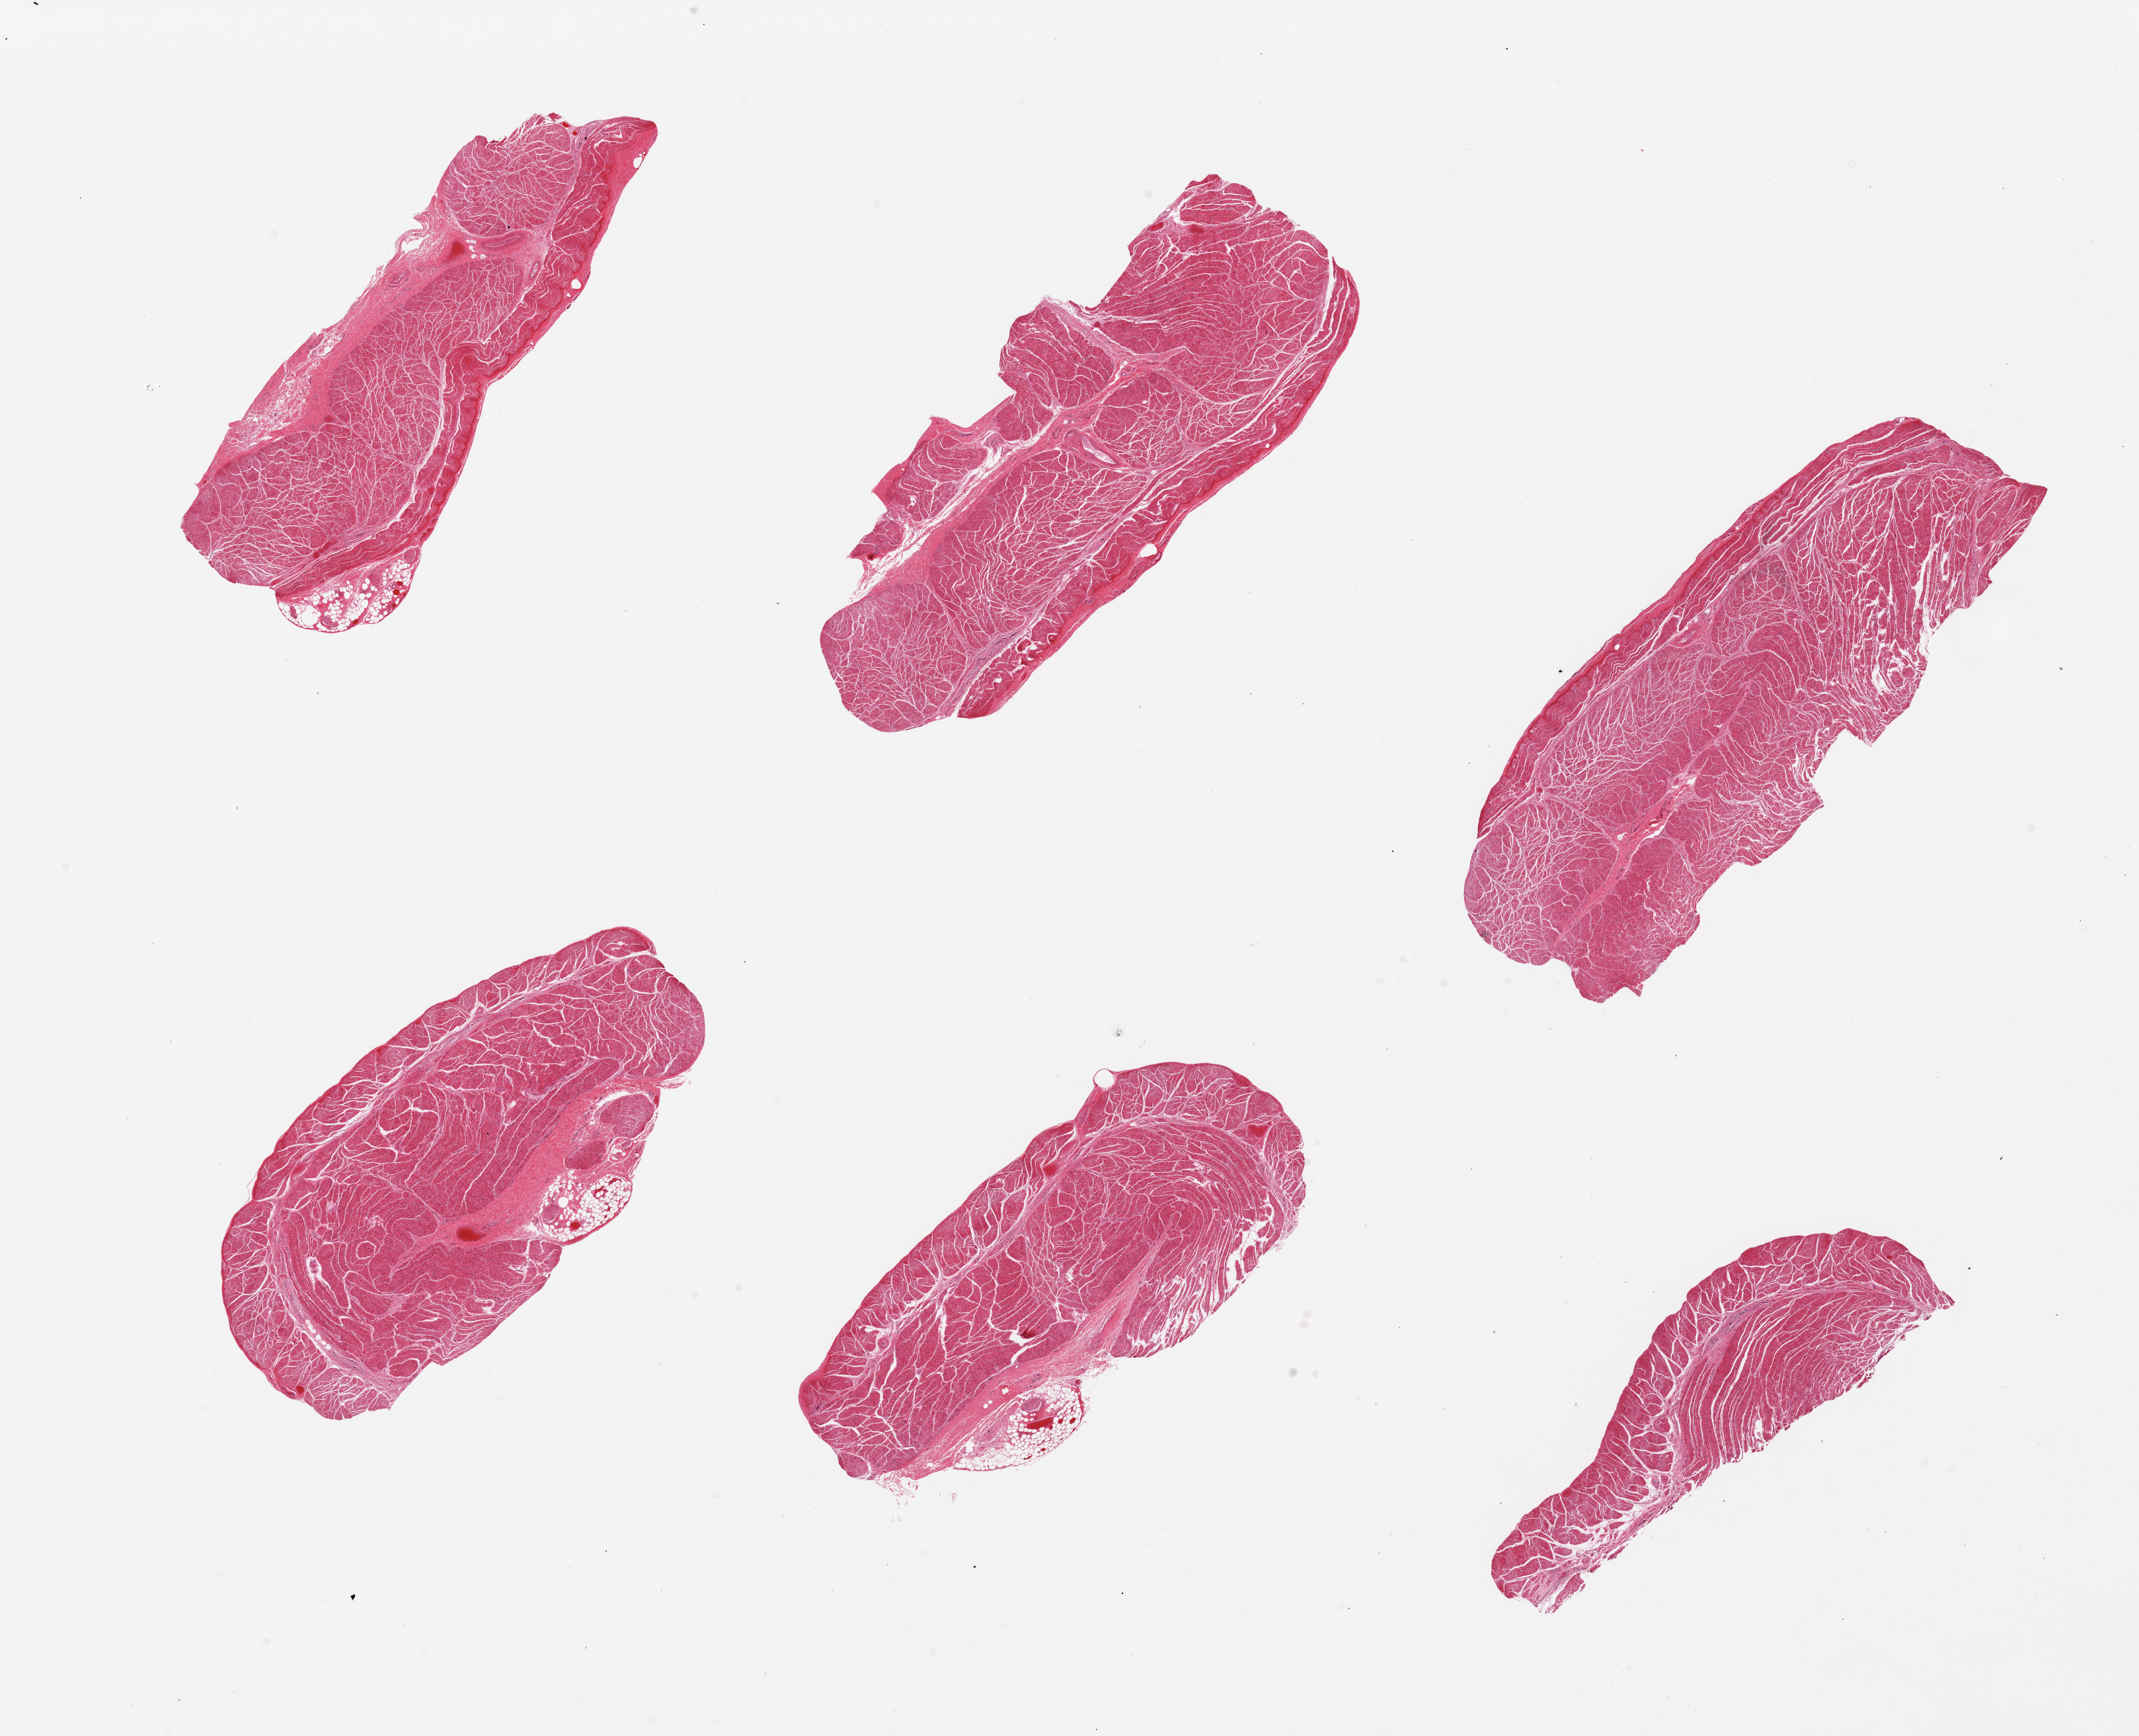
Whole-slide image, hematoxylin and eosin (H&E) stain, brightfield — low-resolution overview of the scanned area, about 25.6 x 20.8 mm. Donor: male.
• specimen: PAXgene-fixed paraffin-embedded (PFPE) section; sampled site (target tissue): esophageal muscle; donor tissue sample